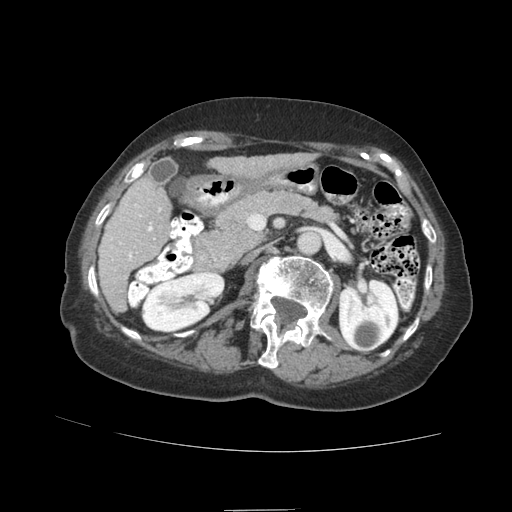
Contrast-enhanced abdominal CT (liver protocol), one axial slice; position 33 of 89 along the scan axis; soft-tissue window (W 400 / L 40 HU); 2.5 mm slice thickness; 512 × 512 image matrix, field of view 360 × 360 mm. Case-level facts recorded for this patient, not image findings: diagnosis: hepatocellular carcinoma (patient treated with transarterial chemoembolisation; whether this scan precedes or follows treatment is not stated here); TNM stage (as recorded): Stage-II; Child-Pugh class: A; tumour differentiation: moderately differentiated; tumour nodularity: multinodular.
Annotated regions visible in this slice (semi-automatic segmentation, software-assisted and operator-edited):
- liver parenchyma outside the tumour (the mass and vessels are separate outlines, so this box may not span the whole liver): bounding box (x1, y1, x2, y2) in pixels: (98, 154, 292, 312)
- liver vessels: (111, 204, 162, 260)